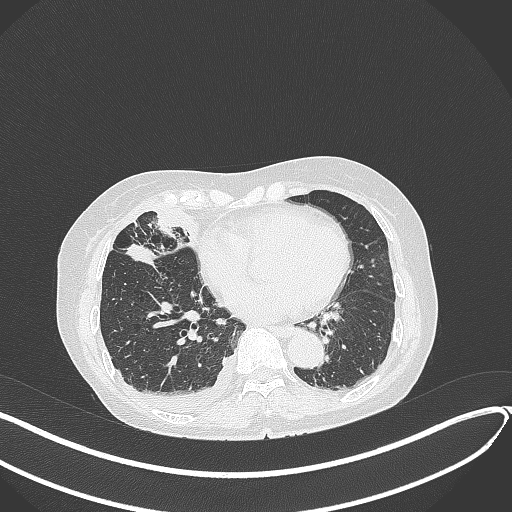
Chest CT, one axial slice. Slice 150 of 418 in the series (ordered by position). 120 kVp. Lung window (W 1500 / L -600 HU). 1 mm slice thickness. 512 × 512 image matrix, field of view 400 × 400 mm. Female patient, age 75 years. From the clinical record (not read from this slice): clinical TNM (as recorded): T2a N3 M0.
Structures marked on this image (rectangle marked by the reading radiologist):
- lung tumour (recorded histology: adenocarcinoma): box from (x=127, y=243) to (x=160, y=268) px